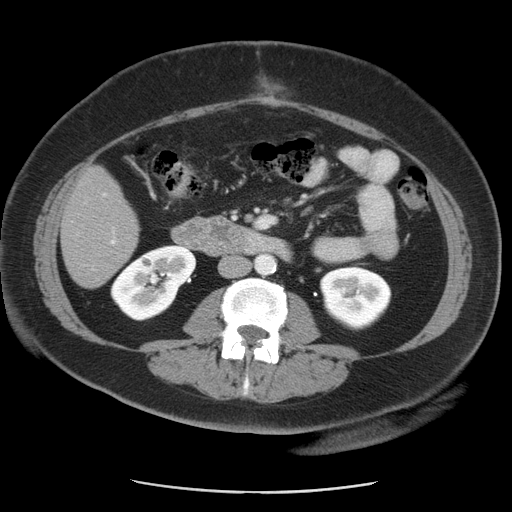
Contrast-enhanced abdominal CT, one axial slice; slice 11 of 55 in the series (ordered by position); 120 kVp; intravenous contrast given; soft-tissue window (W 400 / L 40 HU); 5 mm slice thickness; 512 × 512 image matrix. Female patient, age 52 years. From the clinical record (not read from this slice): diagnosis: colorectal cancer liver metastases, imaged before liver resection; multiple liver metastases: yes; largest metastasis: 2.5 cm; disease in both lobes: yes.
Structures marked on this image (expert manual segmentation):
- liver: bounding box [x1, y1, x2, y2] px = [61, 168, 139, 288]
- planned liver remnant (the part of the liver to remain after resection): [61, 195, 133, 288]
- portal vein (with intrahepatic branches): [76, 192, 118, 272]